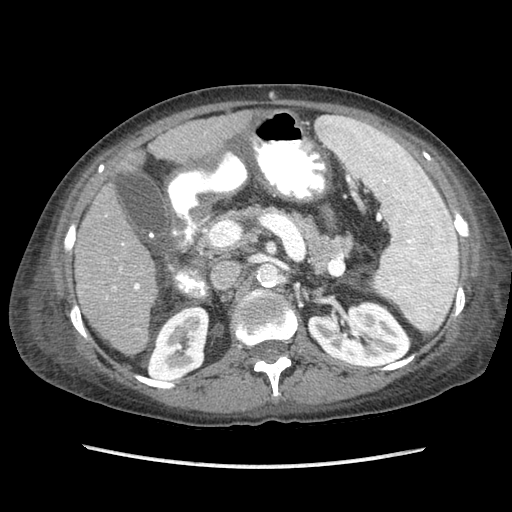
Contrast-enhanced abdominal CT (liver protocol), one axial slice; slice 37 of 87 in the series (ordered by position); reconstruction kernel STANDARD; 120 kVp; soft-tissue window (W 400 / L 40 HU); 2.5 mm slice thickness; 512 × 512 image matrix, field of view 340 × 340 mm. From the clinical record (not read from this slice): diagnosis: hepatocellular carcinoma (patient treated with transarterial chemoembolisation; whether this scan precedes or follows treatment is not stated here); TNM stage (as recorded): Stage-IIIB; Child-Pugh class: A; tumour differentiation: no biopsy; tumour nodularity: uninodular.
Structures marked on this image (semi-automatic segmentation, software-assisted and operator-edited):
- liver parenchyma outside the tumour (the mass and vessels are separate outlines, so this box may not span the whole liver): bounding box [x1, y1, x2, y2] px = [74, 110, 252, 354]
- liver vessels: [106, 243, 140, 330]